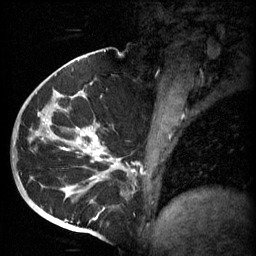
Breast MRI (dynamic contrast-enhanced), one sagittal slice; slice 32 of 60 in the series (ordered by position); 3 images stored at this slice position (order not interpretable as contrast timing); 1.5 T; TE 4.2 ms, TR 11 ms; 2 mm slice thickness; 256 × 256 image matrix, field of view 200 × 200 mm. Patient: female, 51 years.
Annotated regions visible in this slice (semi-automatic segmentation, software-assisted and operator-edited):
- analysis volume of interest (the breast-tissue region the enhancement analysis was run in; not a lesion): bounding box [x1, y1, x2, y2] px = [48, 82, 161, 197]
- tumour enhancement mask (voxels above the 70 % enhancement threshold inside the analysis volume of interest): [52, 92, 137, 197]